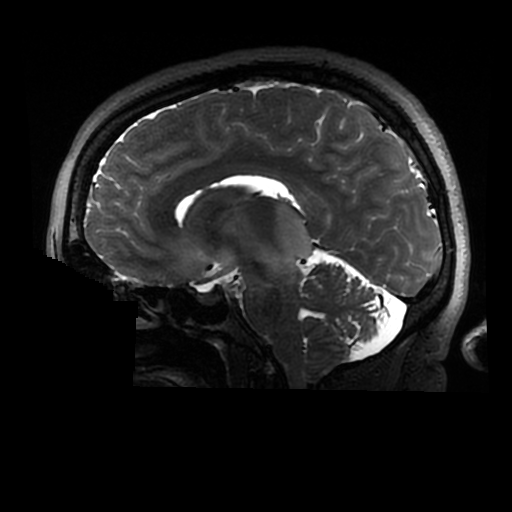
Brain MRI from a brain-tumour surgery series, one sagittal slice; position 166 of 320 along the scan axis; 0.6 mm slice thickness; 512 × 512 image matrix, field of view 240 × 240 mm. Case-level facts recorded for this patient, not image findings: histopathology: Astrocytoma; WHO grade: 2; IDH mutation: yes.
Outlined on this slice (expert manual segmentation):
- tumour: bounding box (x1, y1, x2, y2) in pixels: (270, 203, 314, 269)